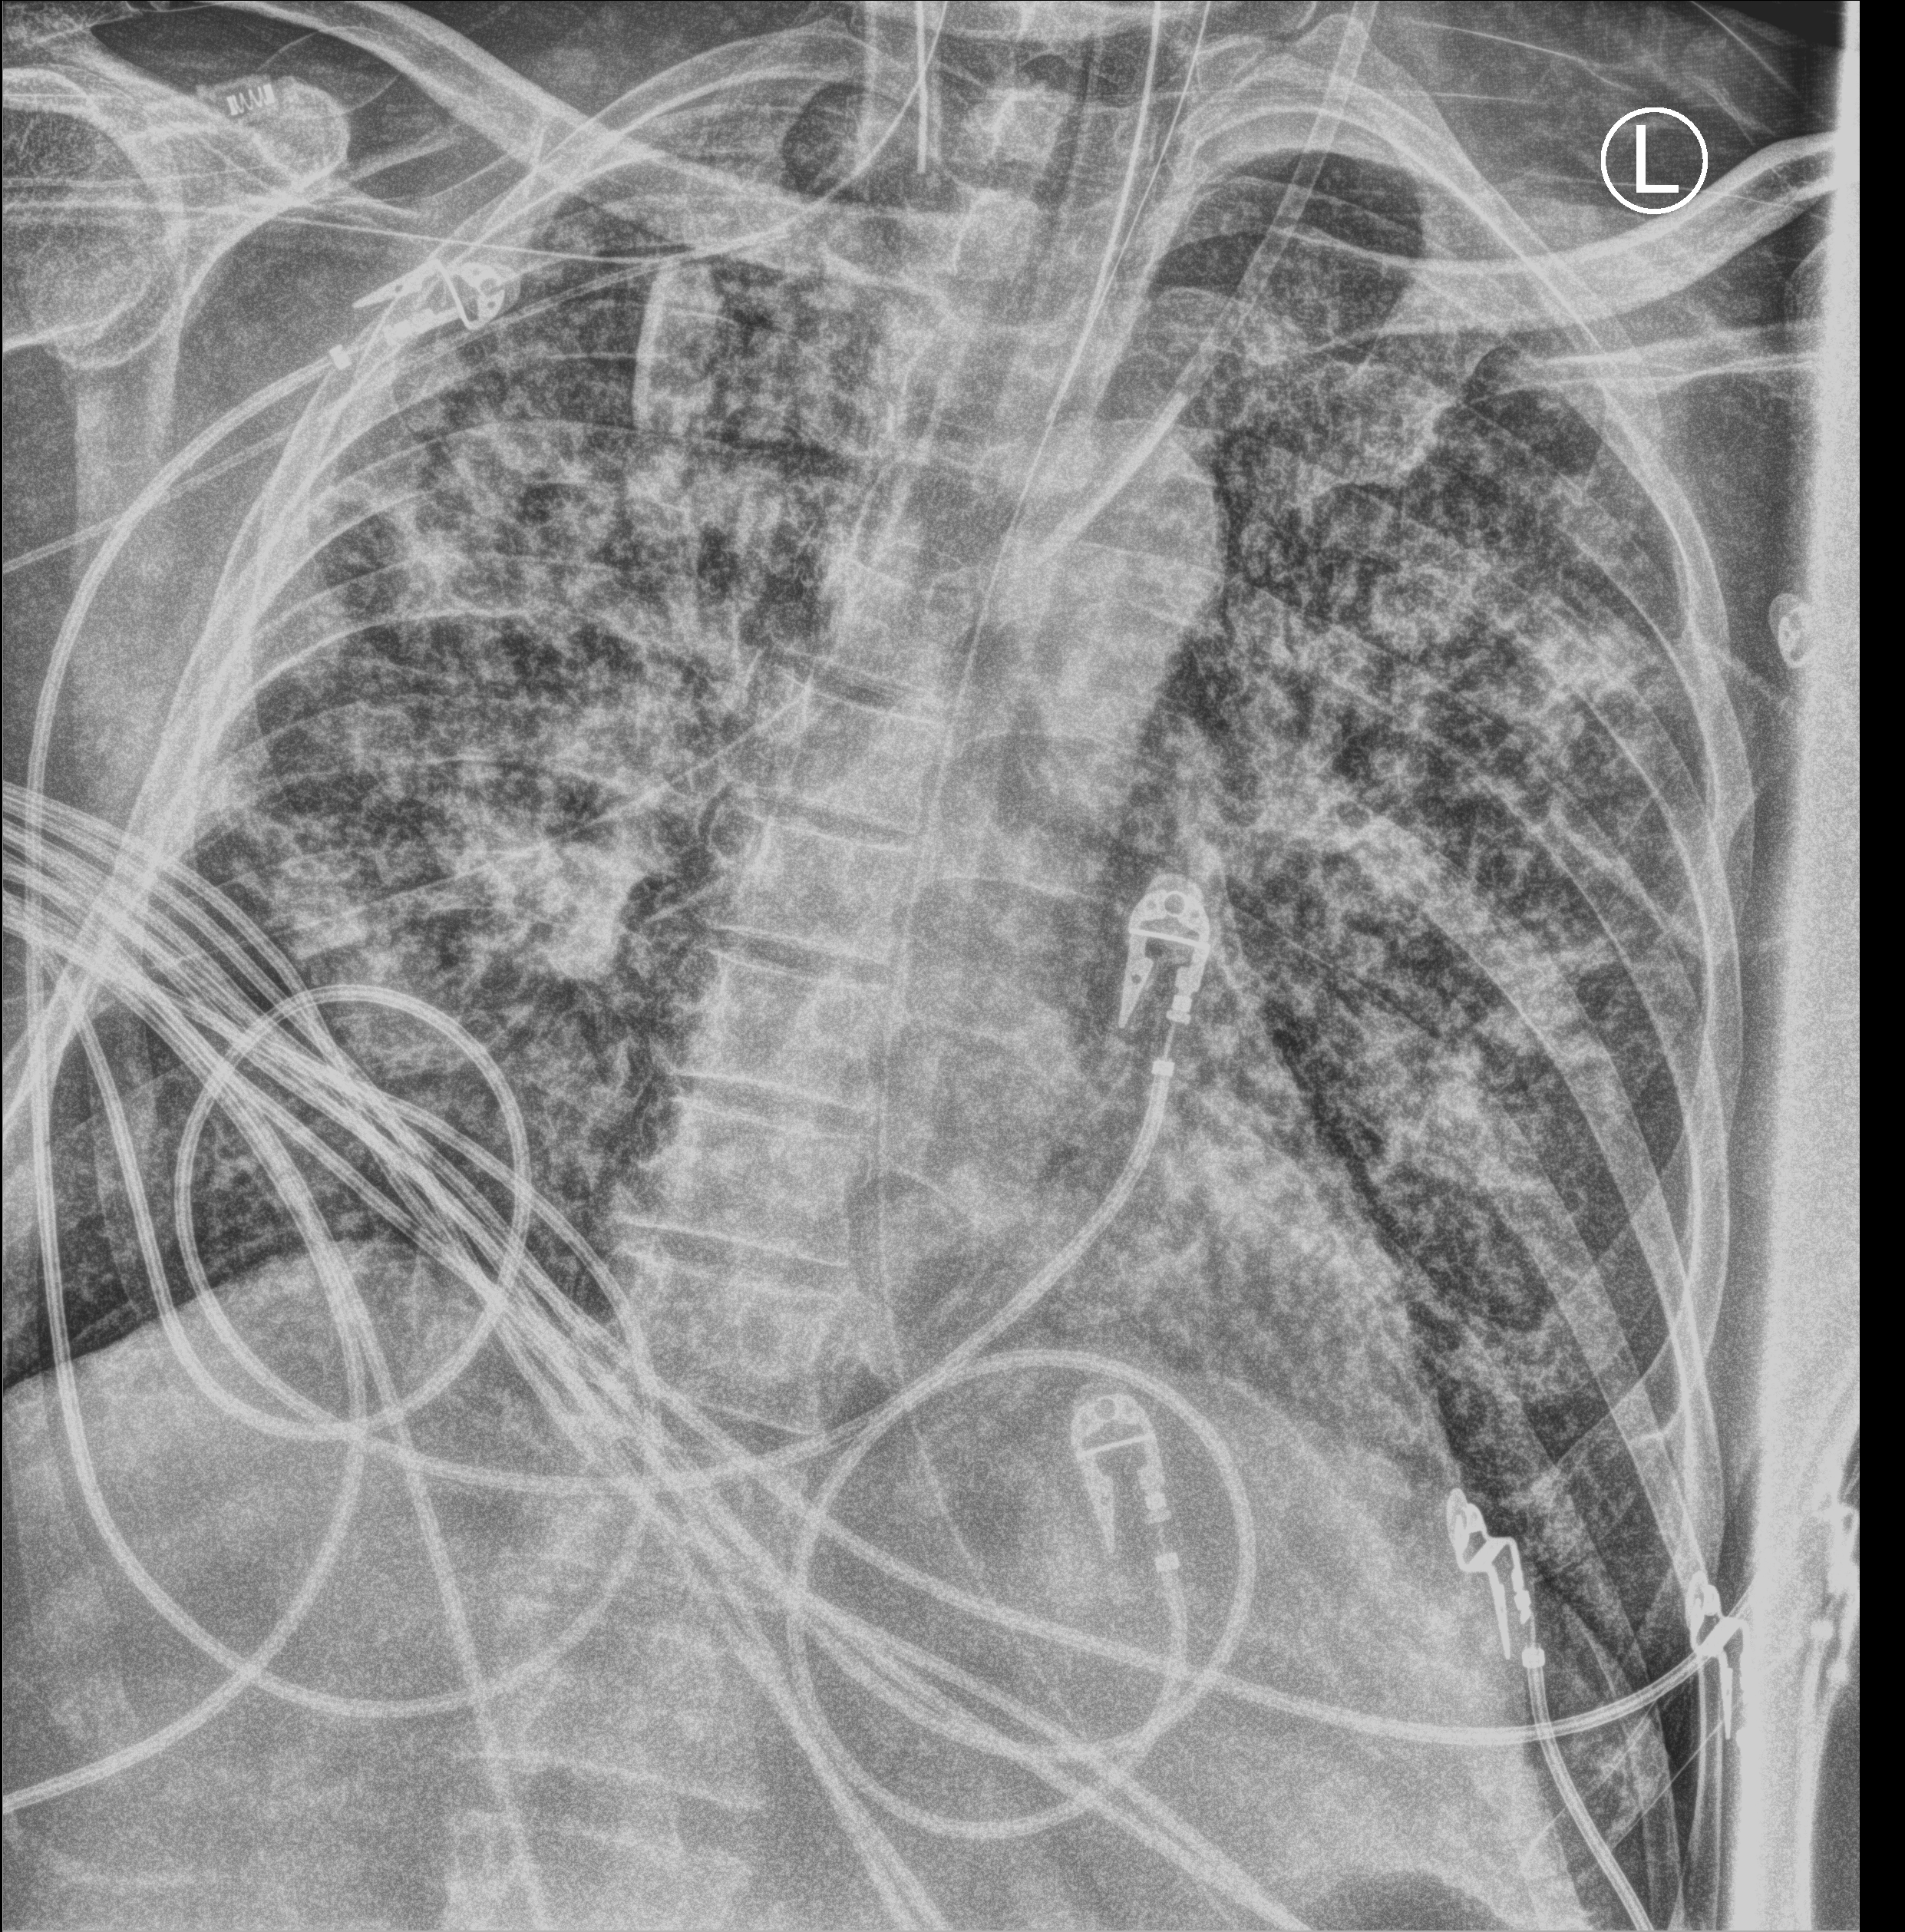
Chest X-ray (portable), anteroposterior (AP) projection. Patient hospitalised with COVID-19; male, aged 60–74 years.
Admission-level facts for this patient (not findings on this image; timing relative to this image not recorded): mechanically ventilated during this hospital stay: yes.